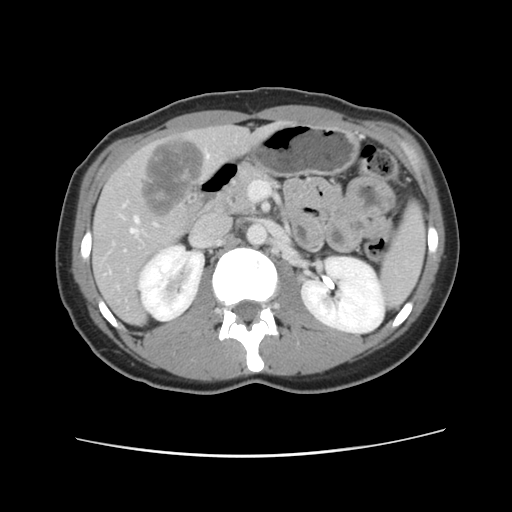
Contrast-enhanced abdominal CT, one axial slice. Position 48 of 134 along the scan axis. 120 kVp. Intravenous contrast given. Soft-tissue window (W 400 / L 40 HU). 2.5 mm slice thickness. 512 × 512 image matrix, field of view 339 × 339 mm. Female patient, age 33 years. Case-level facts recorded for this patient, not image findings: diagnosis: colorectal cancer liver metastases, imaged before liver resection; multiple liver metastases: yes; largest metastasis: 4.5 cm.
Structures marked on this image (expert manual segmentation):
- hepatic veins: bounding box [x1, y1, x2, y2] px = [131, 154, 210, 234]
- liver: [93, 125, 281, 324]
- planned liver remnant (the part of the liver to remain after resection): [92, 125, 281, 324]
- liver metastasis: [139, 141, 206, 220]